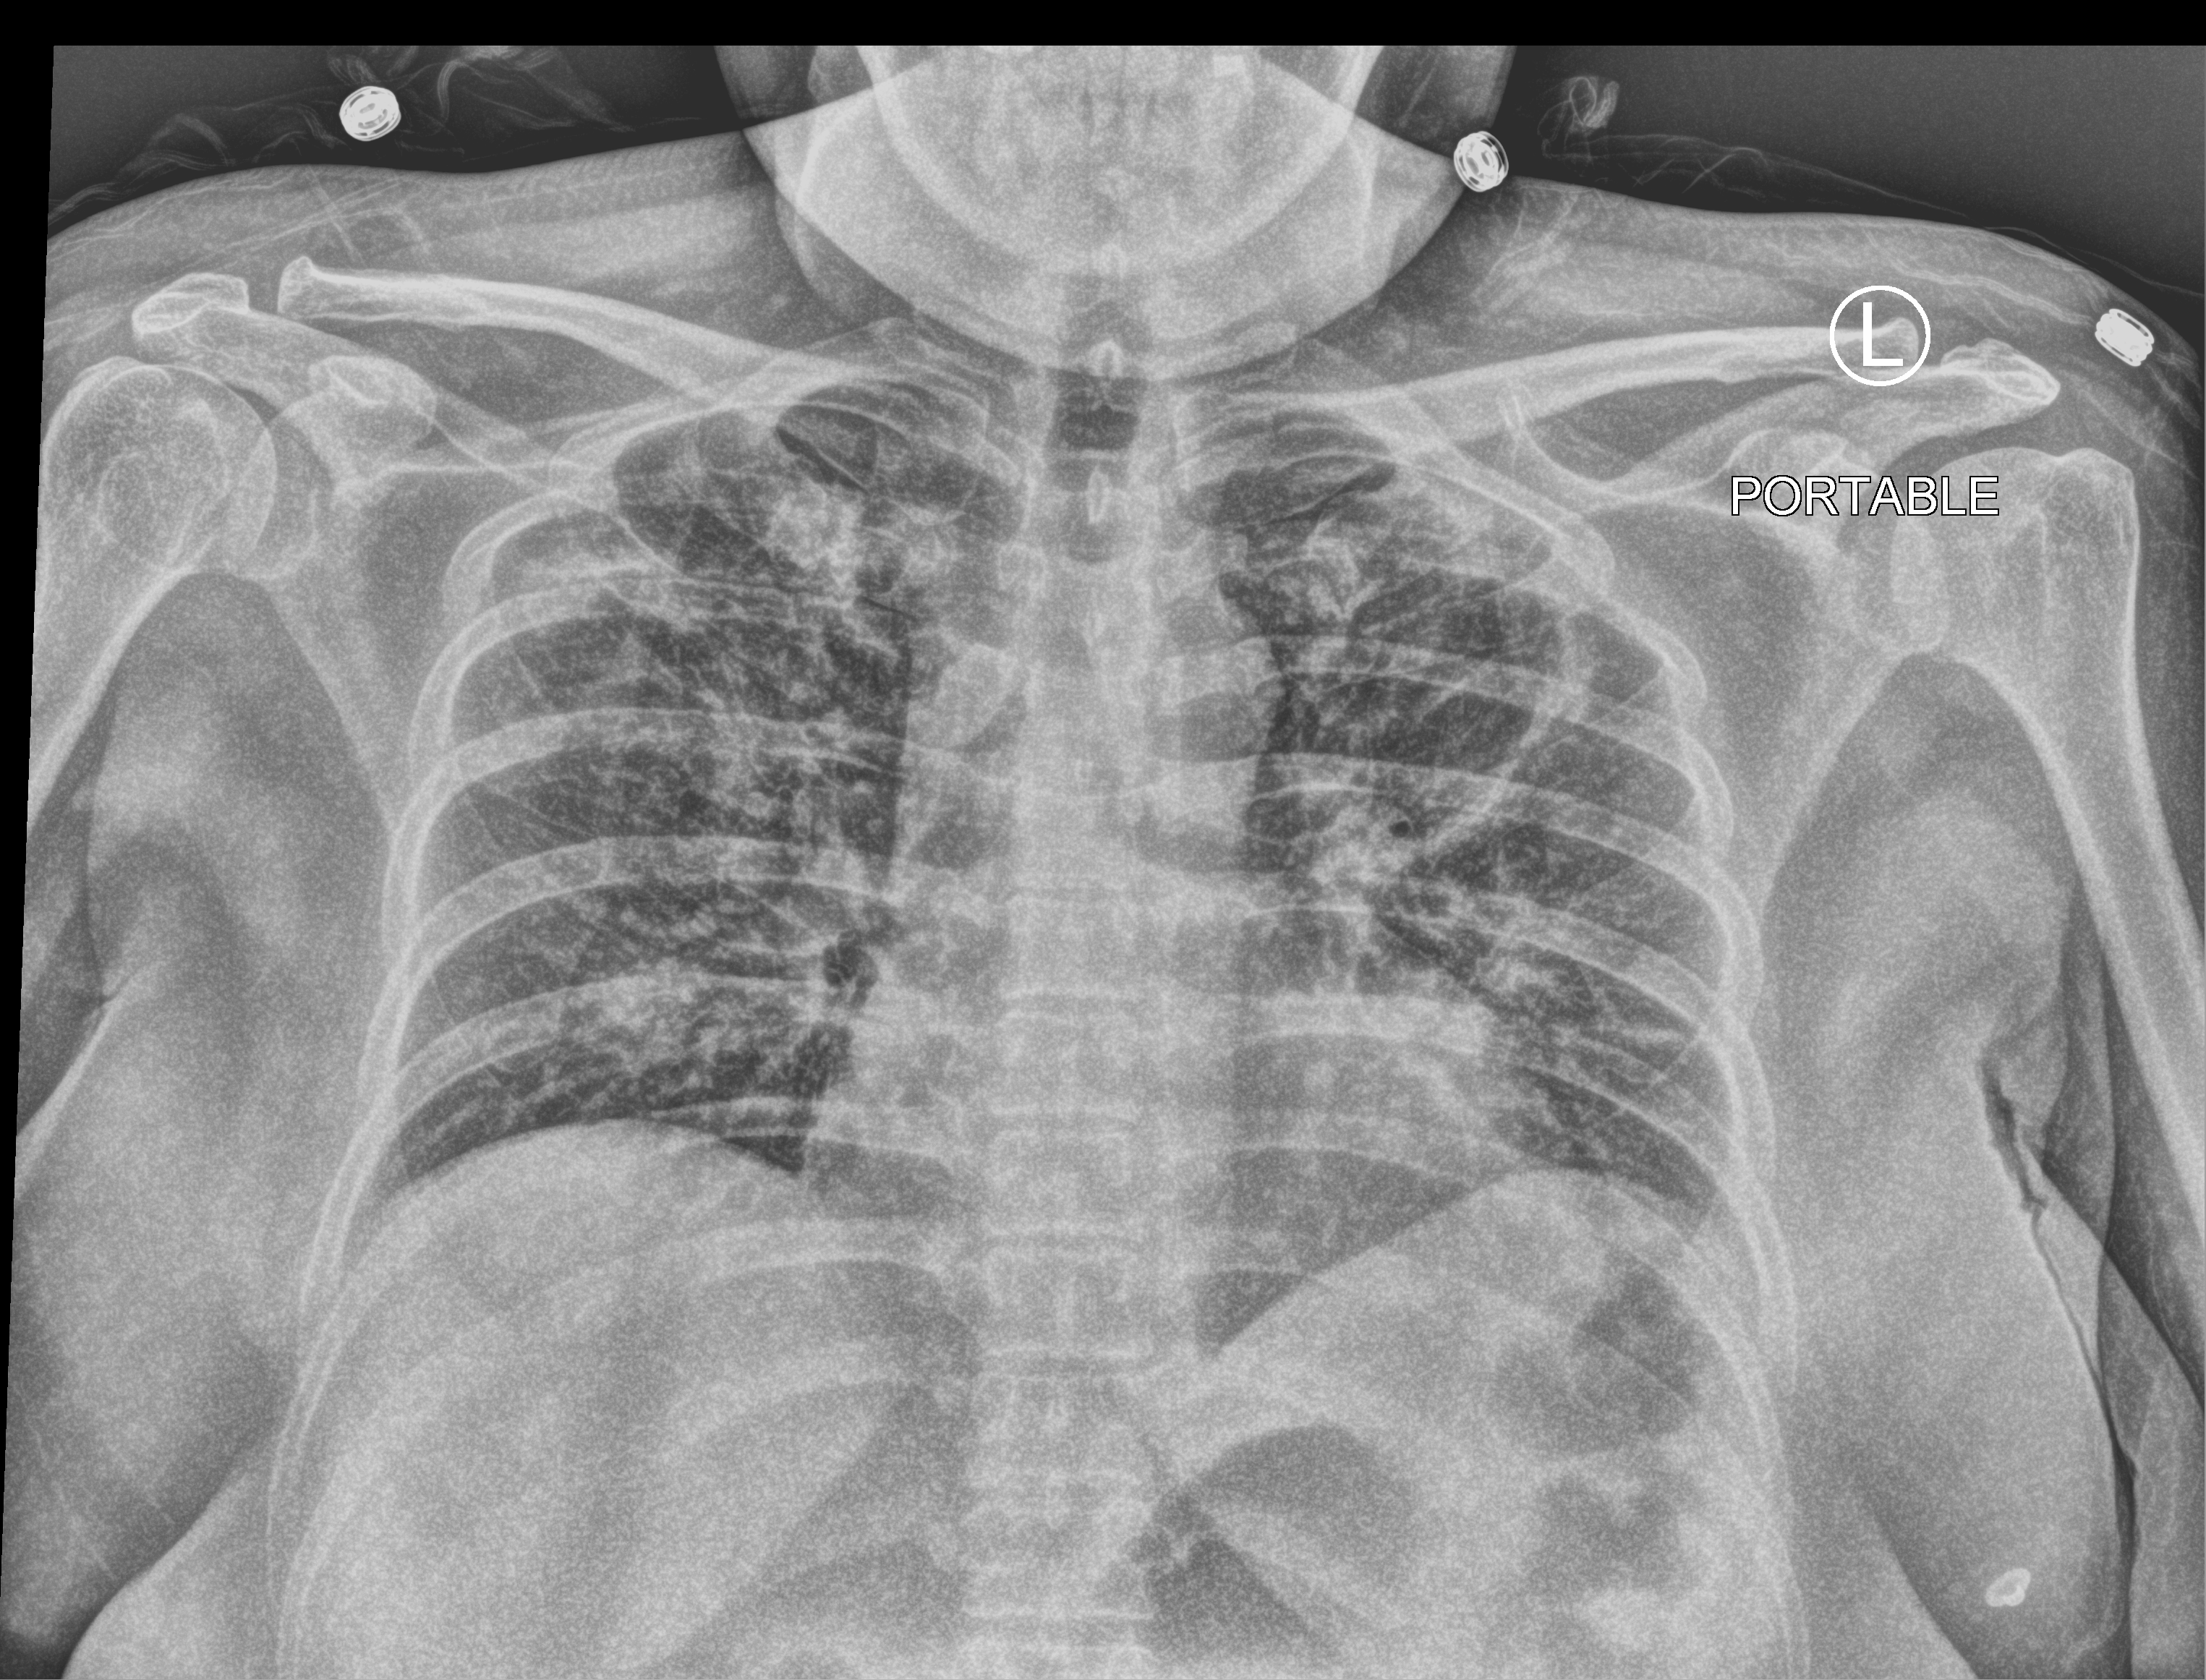
Bedside chest radiograph (computed radiography), anteroposterior (AP) projection. Patient hospitalised with COVID-19; female, aged 18–59 years.
From the hospital-stay record, not from the radiograph (when in the stay this image was taken is not recorded):
- admitted to intensive care during this hospital stay: yes
- mechanically ventilated during this hospital stay: yes